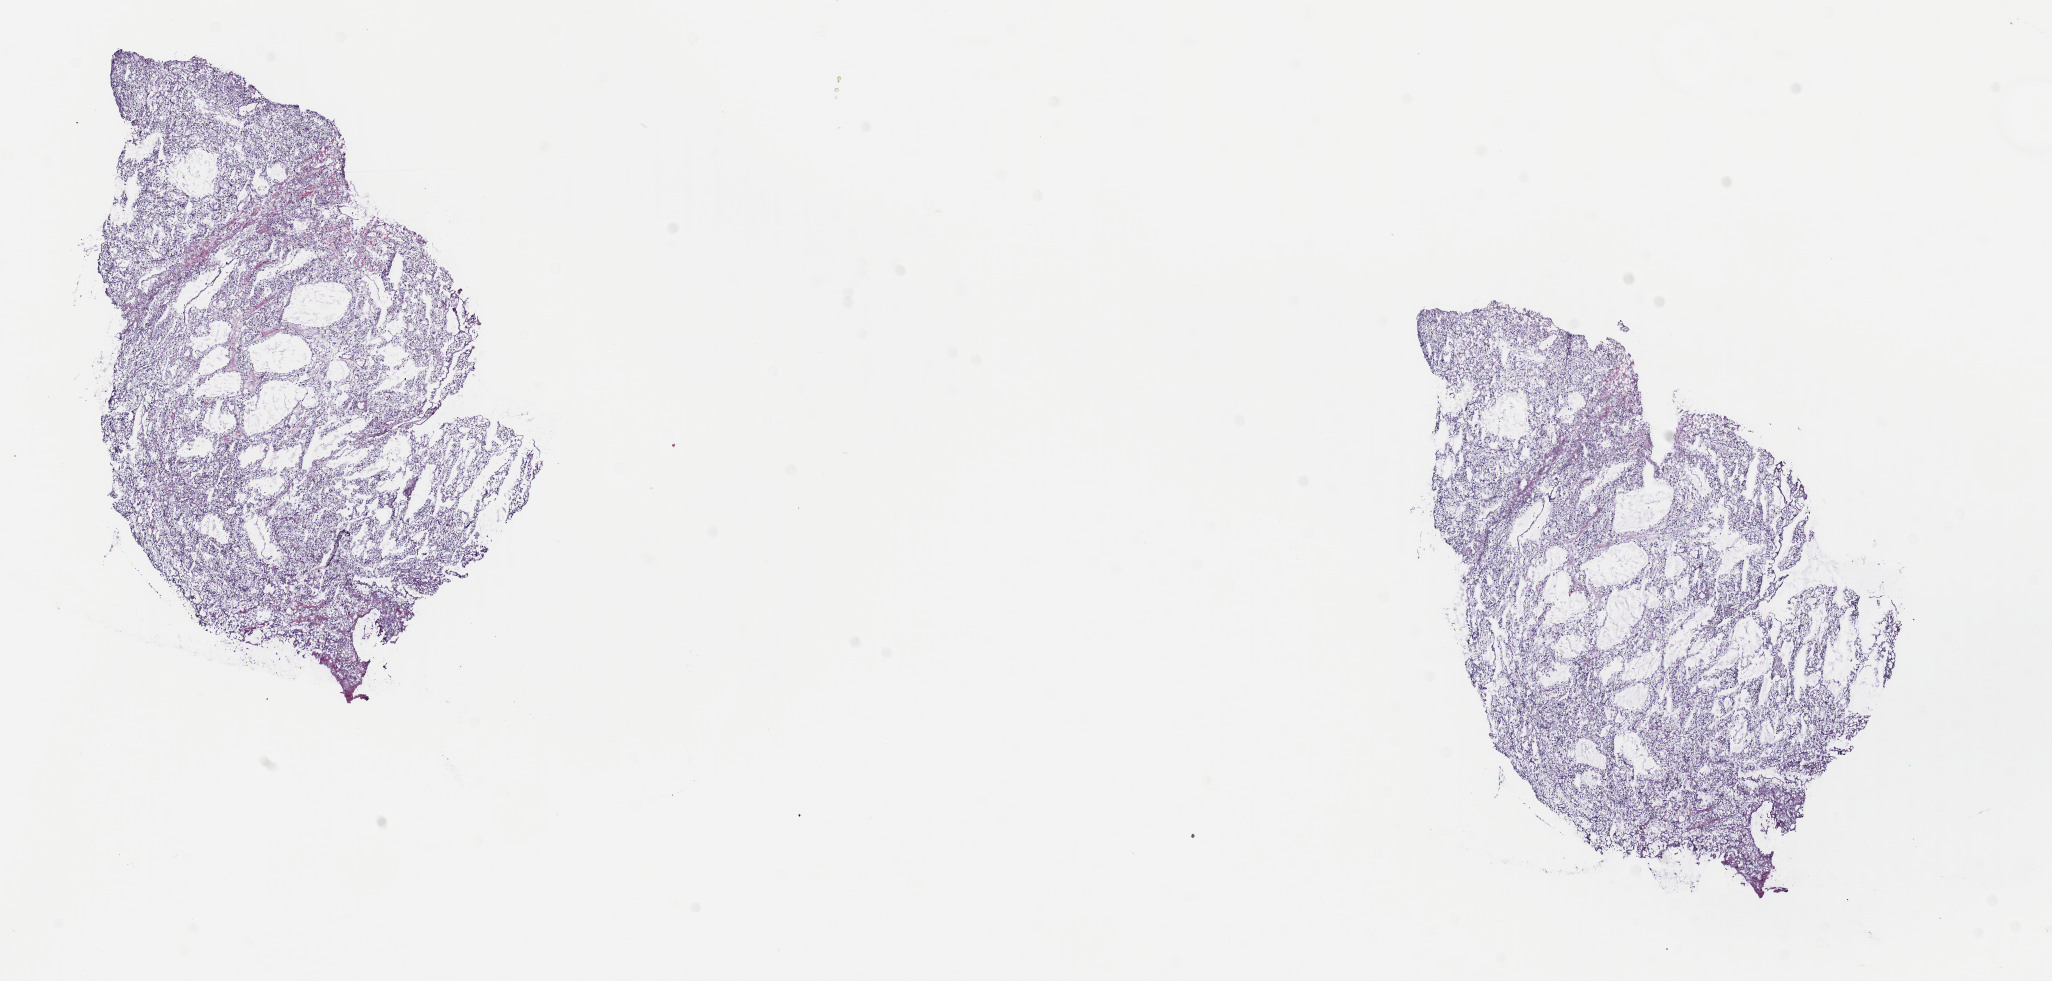
Digitized Hematoxylin and eosin (H&E) stained tissue section (whole slide), whole scanned area (about 16.2 x 7.8 mm) shown as a low-resolution overview, frozen section from the top of the tissue portion, sample: primary tumour, kidney. Female patient; age at initial diagnosis 49 years. Slide review estimates, as recorded: tumour cells 100%, tumour nuclei 95%.
Diagnosis: Renal cell carcinoma, NOS.